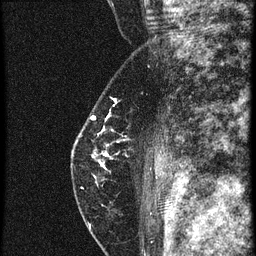
Breast MRI (dynamic contrast-enhanced), one sagittal slice. Position 40 of 60 along the scan axis. 4 images stored at this slice position (order not interpretable as contrast timing). 1.5 T. TE 4.2 ms, TR 20.4 ms. 256 × 256 image matrix, field of view 180 × 180 mm. Patient: female, 46 years. From the clinical record (not read from this slice): setting: breast cancer imaged before/during neoadjuvant chemotherapy; receptor status: triple-negative.
Structures marked on this image (semi-automatically segmented with operator editing):
- analysis volume of interest (the breast-tissue region the enhancement analysis was run in; not a lesion): box from (x=70, y=82) to (x=157, y=201) px
- tumour enhancement mask (voxels above the 90 % enhancement threshold inside the analysis volume of interest): (x=93, y=116)–(x=110, y=167)